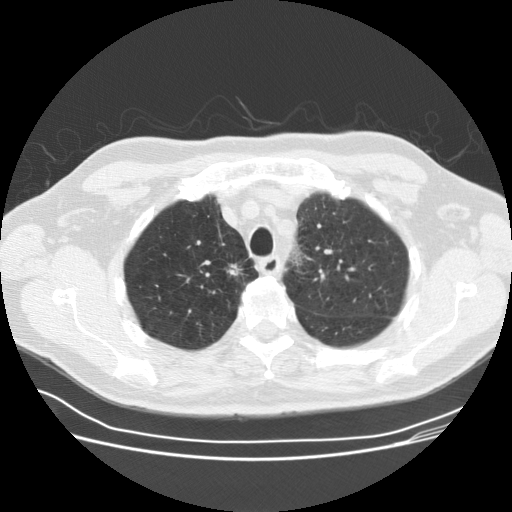
Low-dose screening chest CT, one axial slice; position 127 of 164 along the scan axis; reconstruction kernel STANDARD; 120 kVp; lung window (W 1500 / L -600 HU); 512 × 512 image matrix, field of view 360 × 360 mm.
Annotated regions visible in this slice (expert manual segmentation):
- lesion 1 (tumor, upper lobe of right lung): bounding box [x1, y1, x2, y2] px = [225, 261, 244, 275]